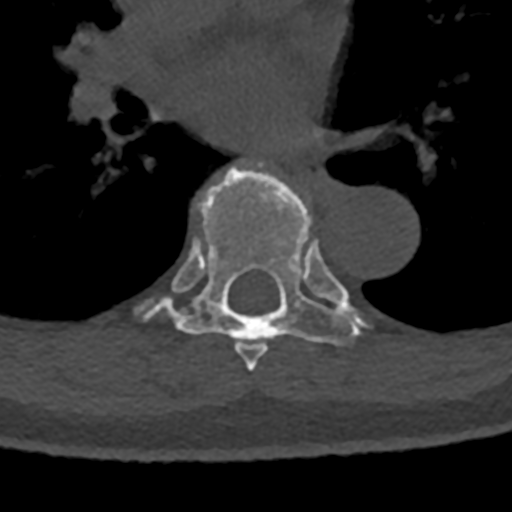
CT including the spine, one axial slice. Slice 772 of 797 in the series (ordered by position). 120 kVp. Bone window (W 1800 / L 400 HU). 0.5 mm slice thickness. 512 × 512 image matrix, field of view 160 × 160 mm. Patient: male, 74 years. From the clinical record (not read from this slice): primary cancer: renal.
Outlined on this slice (semi-automatic segmentation, software-assisted and operator-edited):
- T6 vertebra: bounding box [x1, y1, x2, y2] px = [236, 341, 268, 371]
- T7 vertebra: [135, 164, 369, 357]